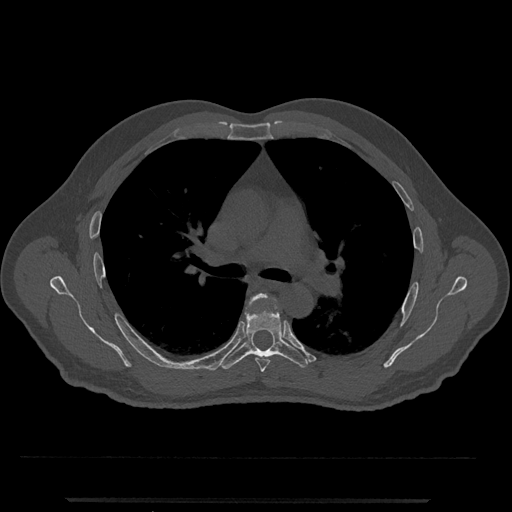
CT including the spine, one axial slice; slice 759 of 797 in the series (ordered by position); reconstruction kernel Br40s/3; 120 kVp; bone window (W 1800 / L 400 HU); 0.5 mm slice thickness; 512 × 512 image matrix, field of view 419 × 419 mm. Patient: male, 63 years. From the clinical record (not read from this slice): primary cancer: prostate.
Outlined on this slice (semi-automatic segmentation, software-assisted and operator-edited):
- T5 vertebra: box from (x=245, y=294) to (x=270, y=372) px
- T6 vertebra: (x=220, y=294)–(x=309, y=370)